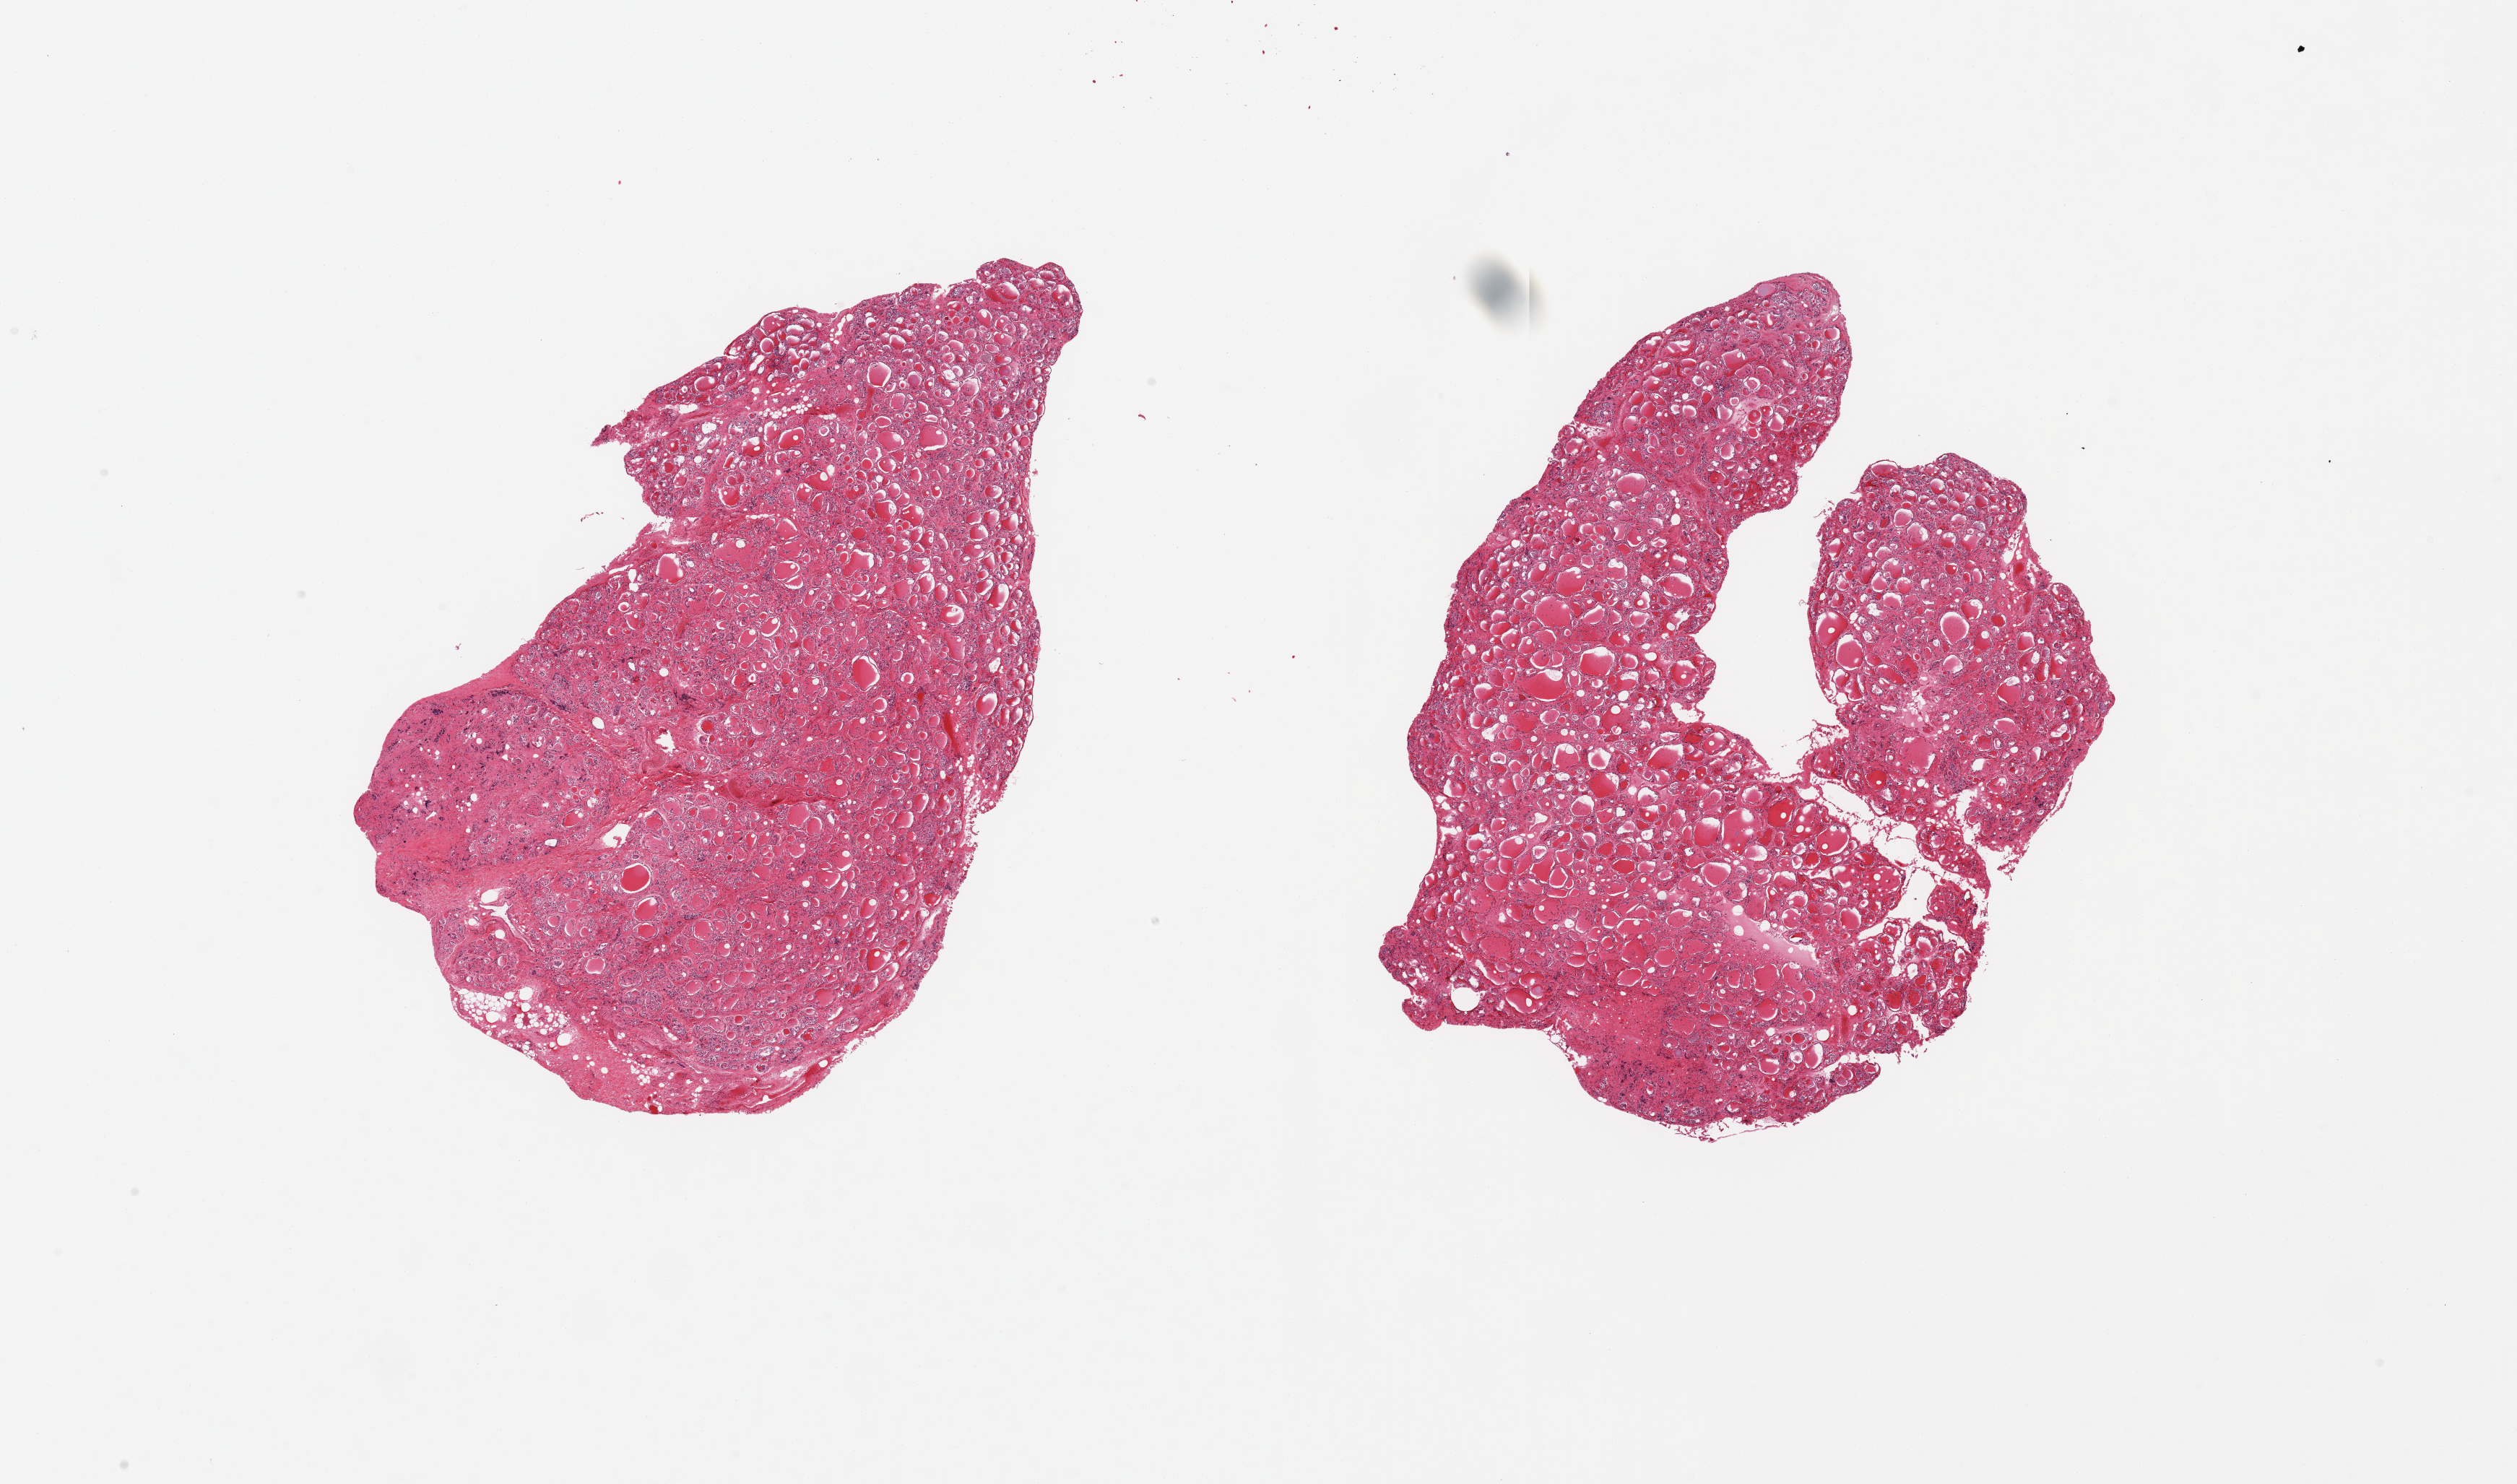
Digitized hematoxylin and eosin (H&E)-stained section, brightfield, a low-resolution overview of the entire scanned area, about 27.6 x 16.3 mm. PAXgene-fixed, paraffin-embedded tissue. Sampled site (target tissue): thyroid. Tissue donor sample. Donor: male.
Review note (as recorded): 2 pieces, mild goitrous changes.